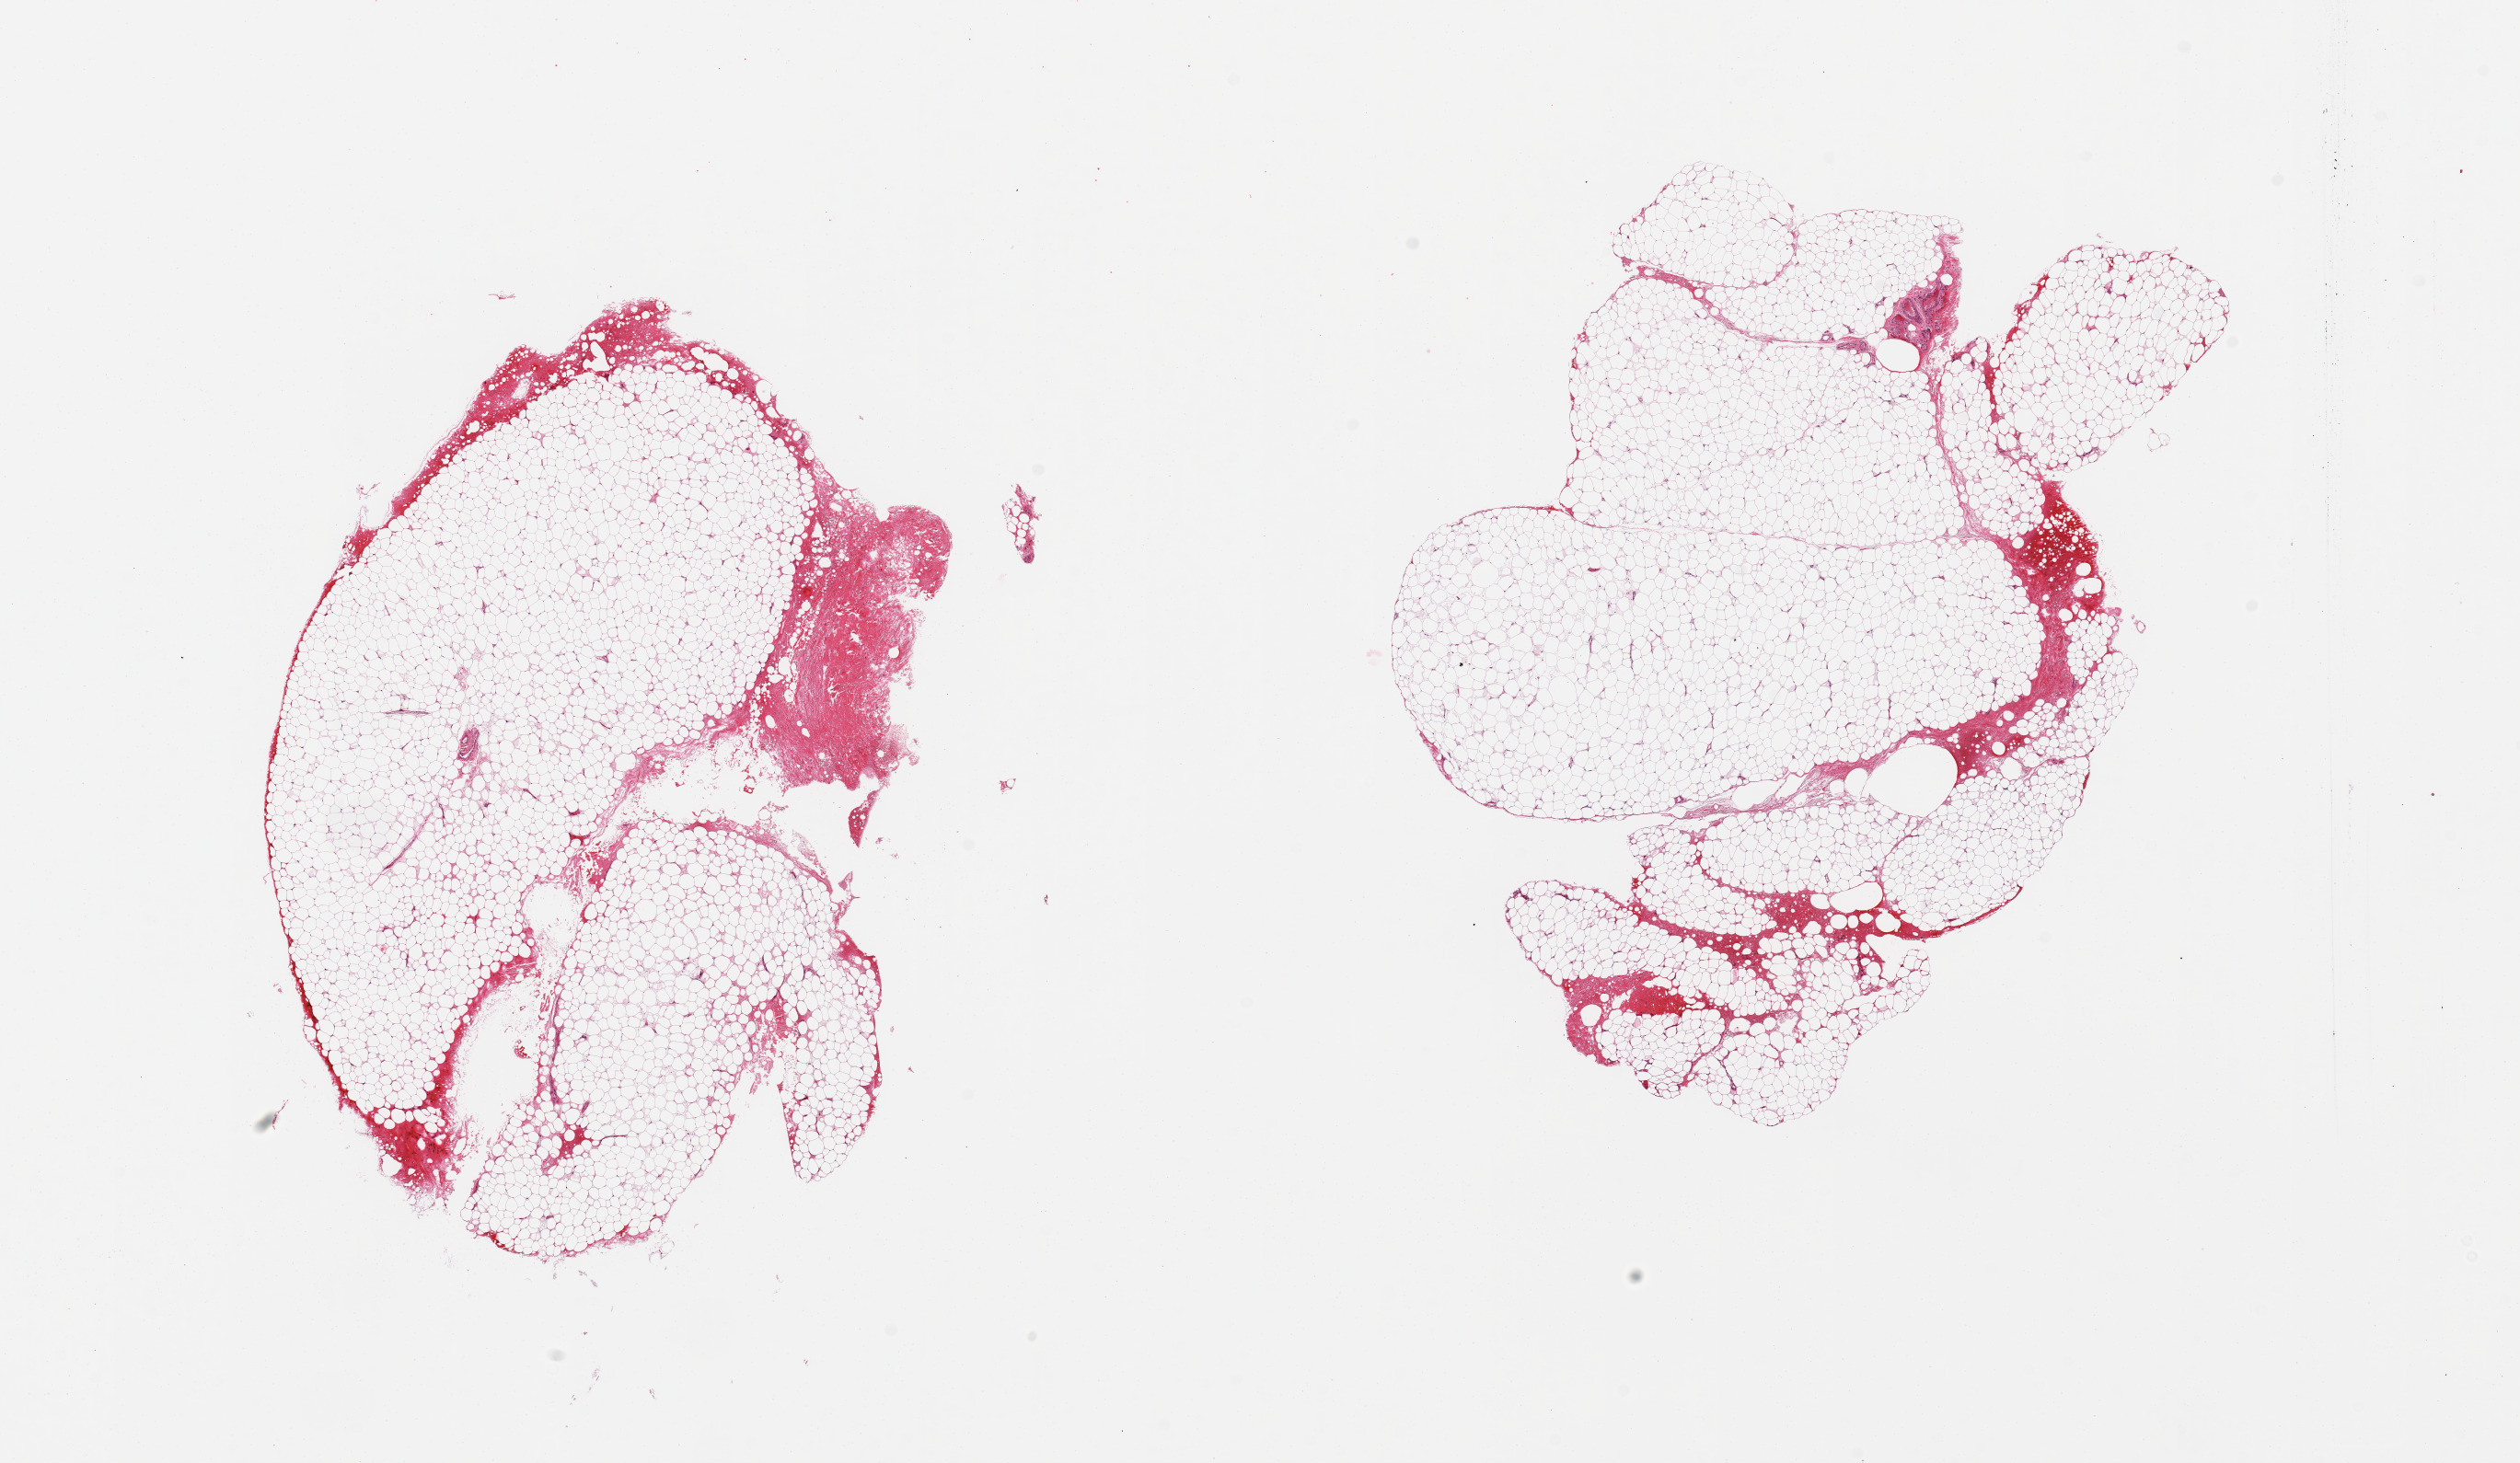
Digitized H&E-stained section, shown as a low-resolution overview of the whole scanned area (about 21.7 x 12.6 mm). PAXgene-fixed paraffin-embedded (PFPE) section. Target tissue: adipose tissue. Donor tissue sample.
Review note (as recorded): 2 pieces, ~10% fascia/vascular elements.